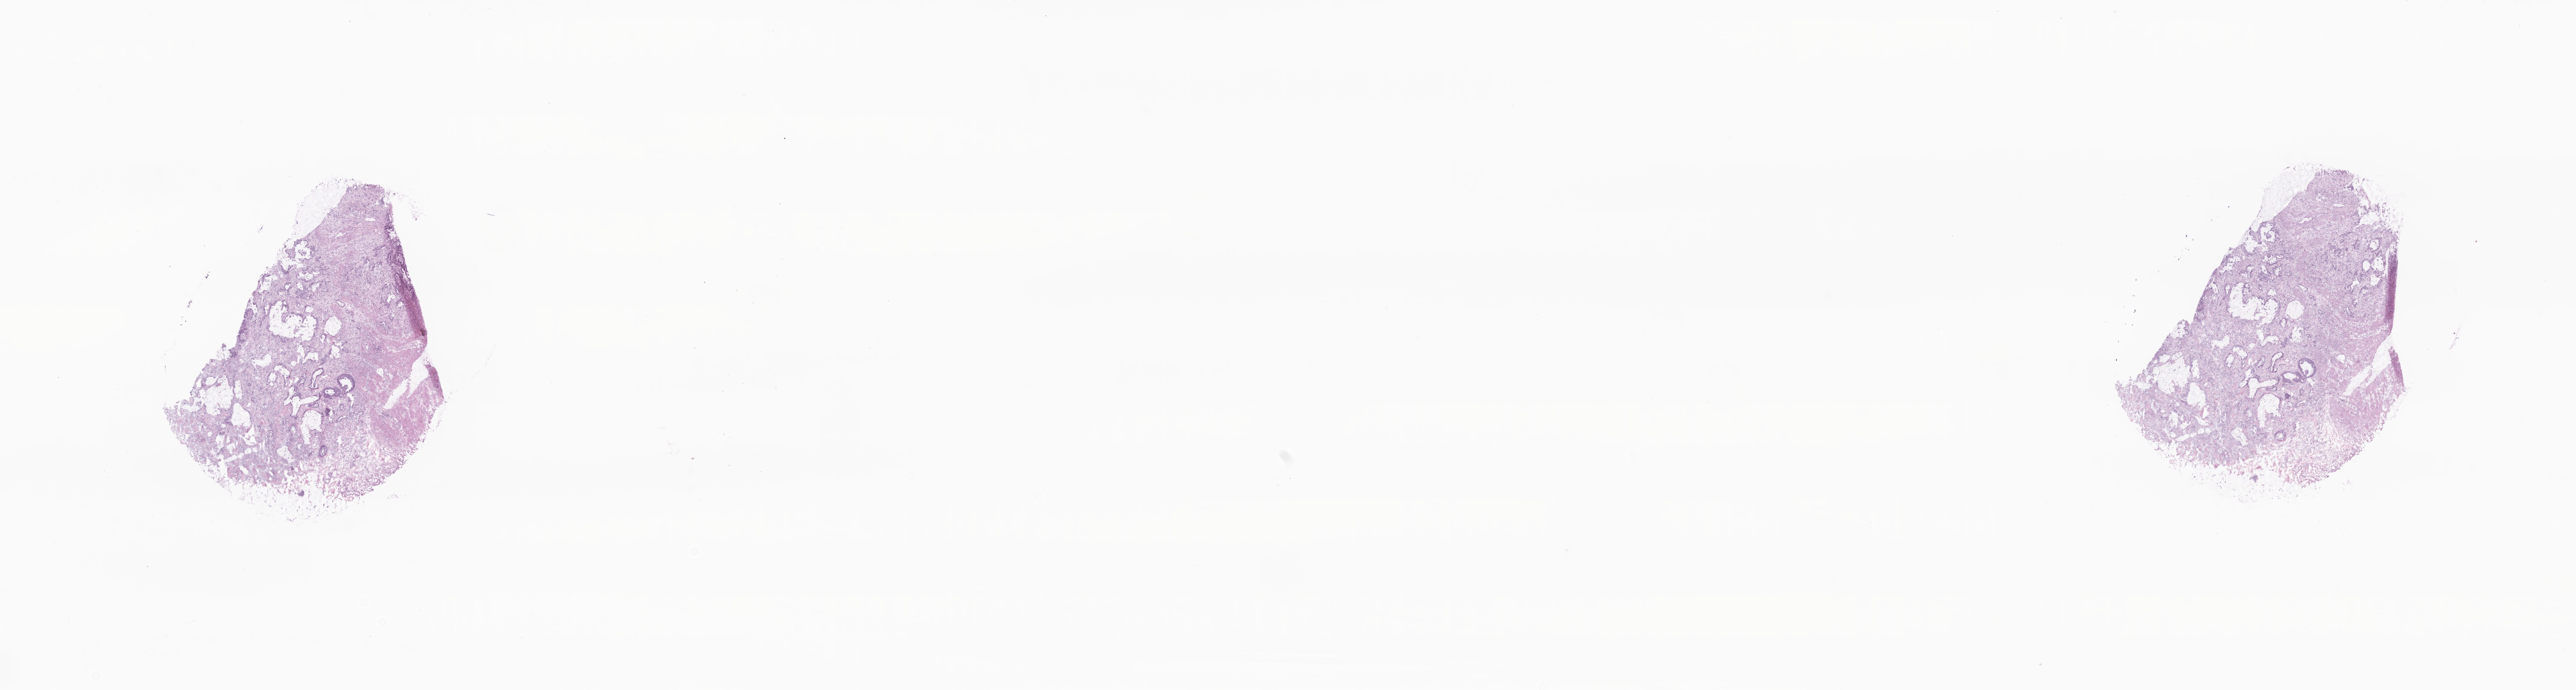
Whole-slide image, hematoxylin and eosin (H&E) stain, low-resolution overview of the scanned area, about 28.7 x 7.7 mm. Frozen section (tissue freezing medium). Primary tumor. Site: ascending colon. Male patient; age at initial diagnosis 62 years. Composition of this section per pathologist review: tumor cells 75%, tumor nuclei 75%, stromal cells 23%, necrosis 2%, normal cells 0%. Inflammatory infiltration, as recorded: lymphocyte infiltration 5%, monocyte infiltration 2%, neutrophil infiltration 7%.
* diagnosis: Mucinous adenocarcinoma
* section: bottom of the tissue portion